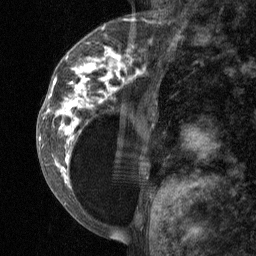
Breast MRI (dynamic contrast-enhanced), one sagittal slice; slice 22 of 64 in the series (ordered by position); dynamic contrast-enhanced study with each time point stored as its own series, time point 2 of 3 at this slice position (early post-contrast, ordered by acquisition time); 1.5 T; TE 4.8 ms, TR 27 ms; 2 mm slice thickness; 256 × 256 image matrix. Patient: female, 34 years. From the clinical record (not read from this slice): setting: breast cancer imaged before/during neoadjuvant chemotherapy; receptor status: HR-positive, HER2-negative.
Structures marked on this image (semi-automatically segmented with operator editing):
- analysis volume of interest (the breast-tissue region the enhancement analysis was run in; not a lesion): box from (x=41, y=23) to (x=157, y=197) px
- tumour enhancement mask (voxels above the 90 % enhancement threshold inside the analysis volume of interest): (x=45, y=46)–(x=145, y=182)